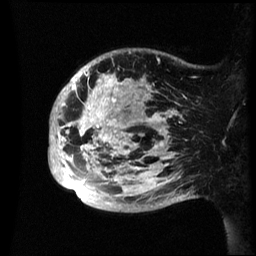
Breast MRI (dynamic contrast-enhanced), one sagittal slice; position 13 of 60 along the scan axis; dynamic contrast-enhanced series, image 2 of 3 at this slice position (ordered by acquisition); 1.5 T; TE 4.2 ms, TR 8.4 ms; 2.4 mm slice thickness; 256 × 256 image matrix, field of view 230 × 230 mm. Female patient, age 48 years.
Annotated regions visible in this slice (semi-automatically segmented with operator editing):
- analysis volume of interest (the breast-tissue region the enhancement analysis was run in; not a lesion): box from (x=49, y=49) to (x=195, y=212) px
- tumour enhancement mask (voxels above the 70 % enhancement threshold inside the analysis volume of interest): (x=49, y=72)–(x=182, y=196)